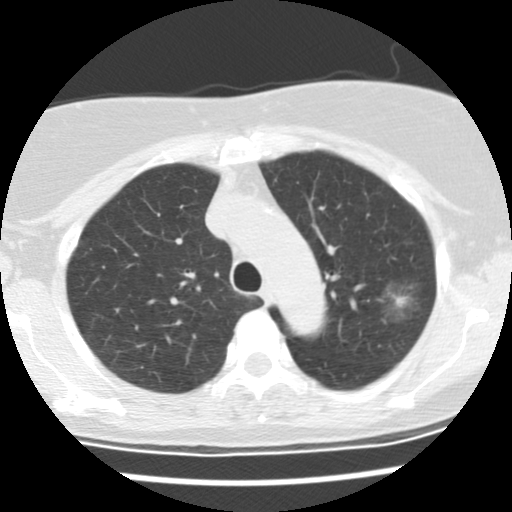
Chest CT (low-dose screening protocol), one axial image; baseline screening round; lung window (W 1500 / L -600 HU); 2.5 mm slice thickness; standard (soft-tissue) reconstruction kernel (STANDARD); slice 105 of 137 in the series; 512 × 512 image matrix, field of view 288 × 288 mm. Female participant, aged 66 years at enrolment. Former smoker at enrolment.
Expert-annotated lung lesion, bounding box [x1, y1, x2, y2] px = [378, 278, 427, 324]. Screening reader's record for this exam (one nodule recorded; not confirmed to be the boxed lesion): non-calcified nodule or mass ≥4 mm, left upper lobe, 25 × 17 mm, poorly defined margins, mixed attenuation.